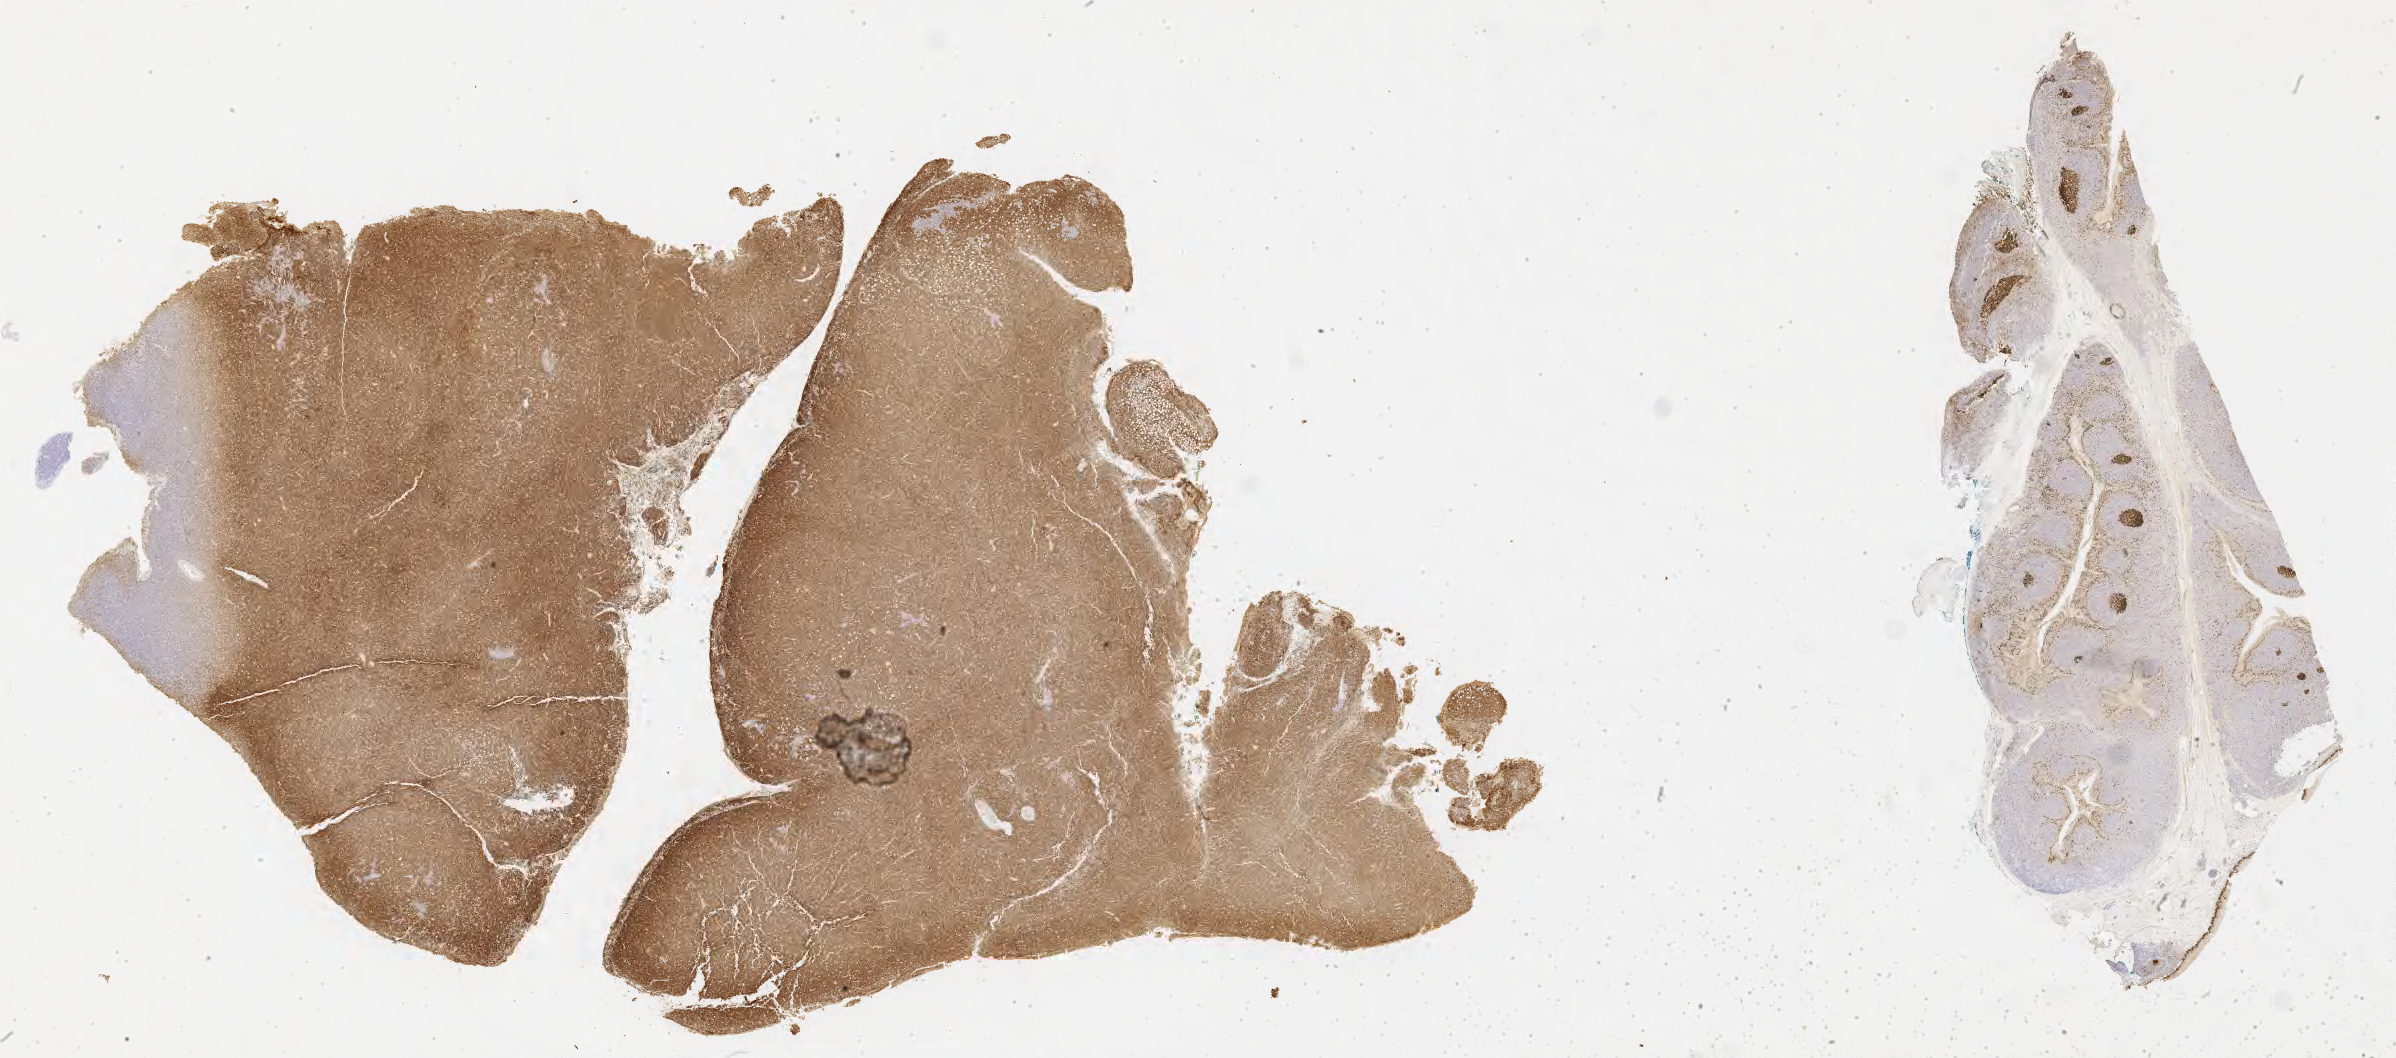
Immunohistochemistry (IHC) whole-slide image stained for Ki-67 — whole scanned area (about 38.7 x 17.1 mm) shown as a low-resolution overview, specimen: tumor tissue, site: peritoneum. Male patient; age at initial diagnosis 9 years.
* histologic diagnosis: Burkitt lymphoma, NOS